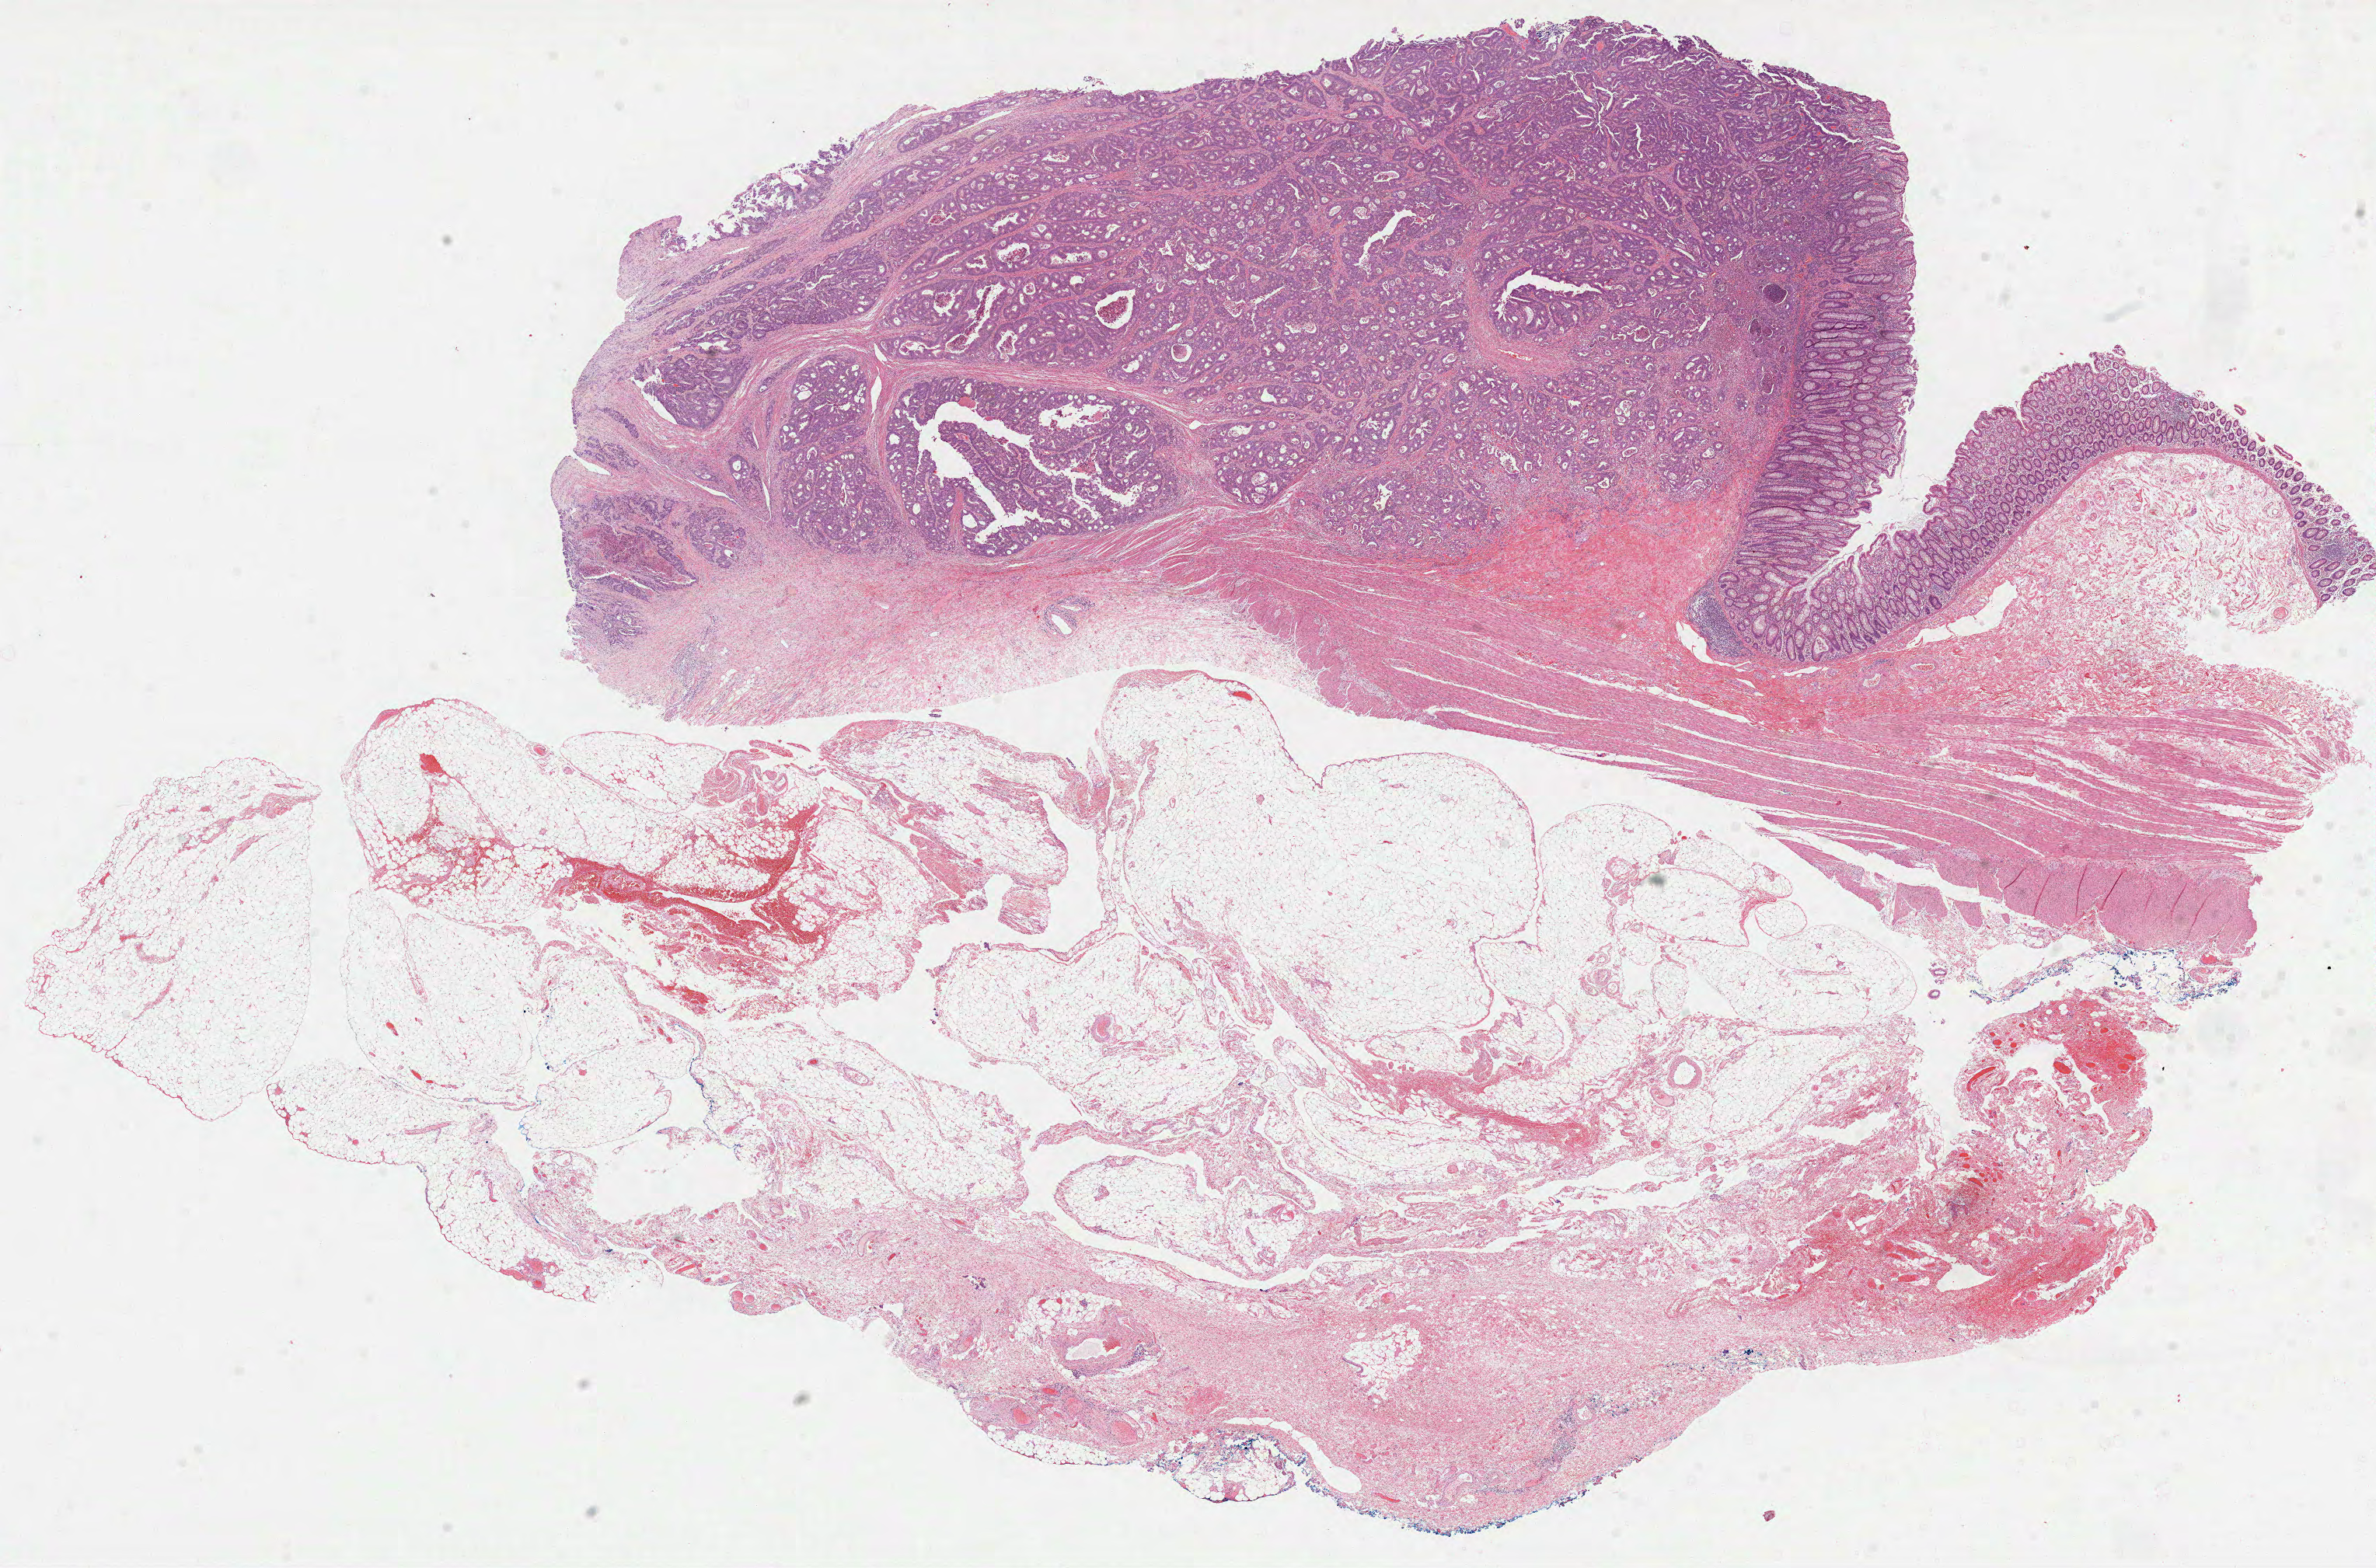
Digitized Hematoxylin and eosin (H&E) stained tissue section (whole slide) — shown as a low-resolution overview of the whole scanned area (about 24.7 x 16.3 mm, acquisition: 40x scan). FFPE section. Primary tumour sample from the colon. Male patient.
AJCC pathologic stage: IIA (6th edition). Pathologic diagnosis: Adenocarcinoma, NOS (ascending colon).